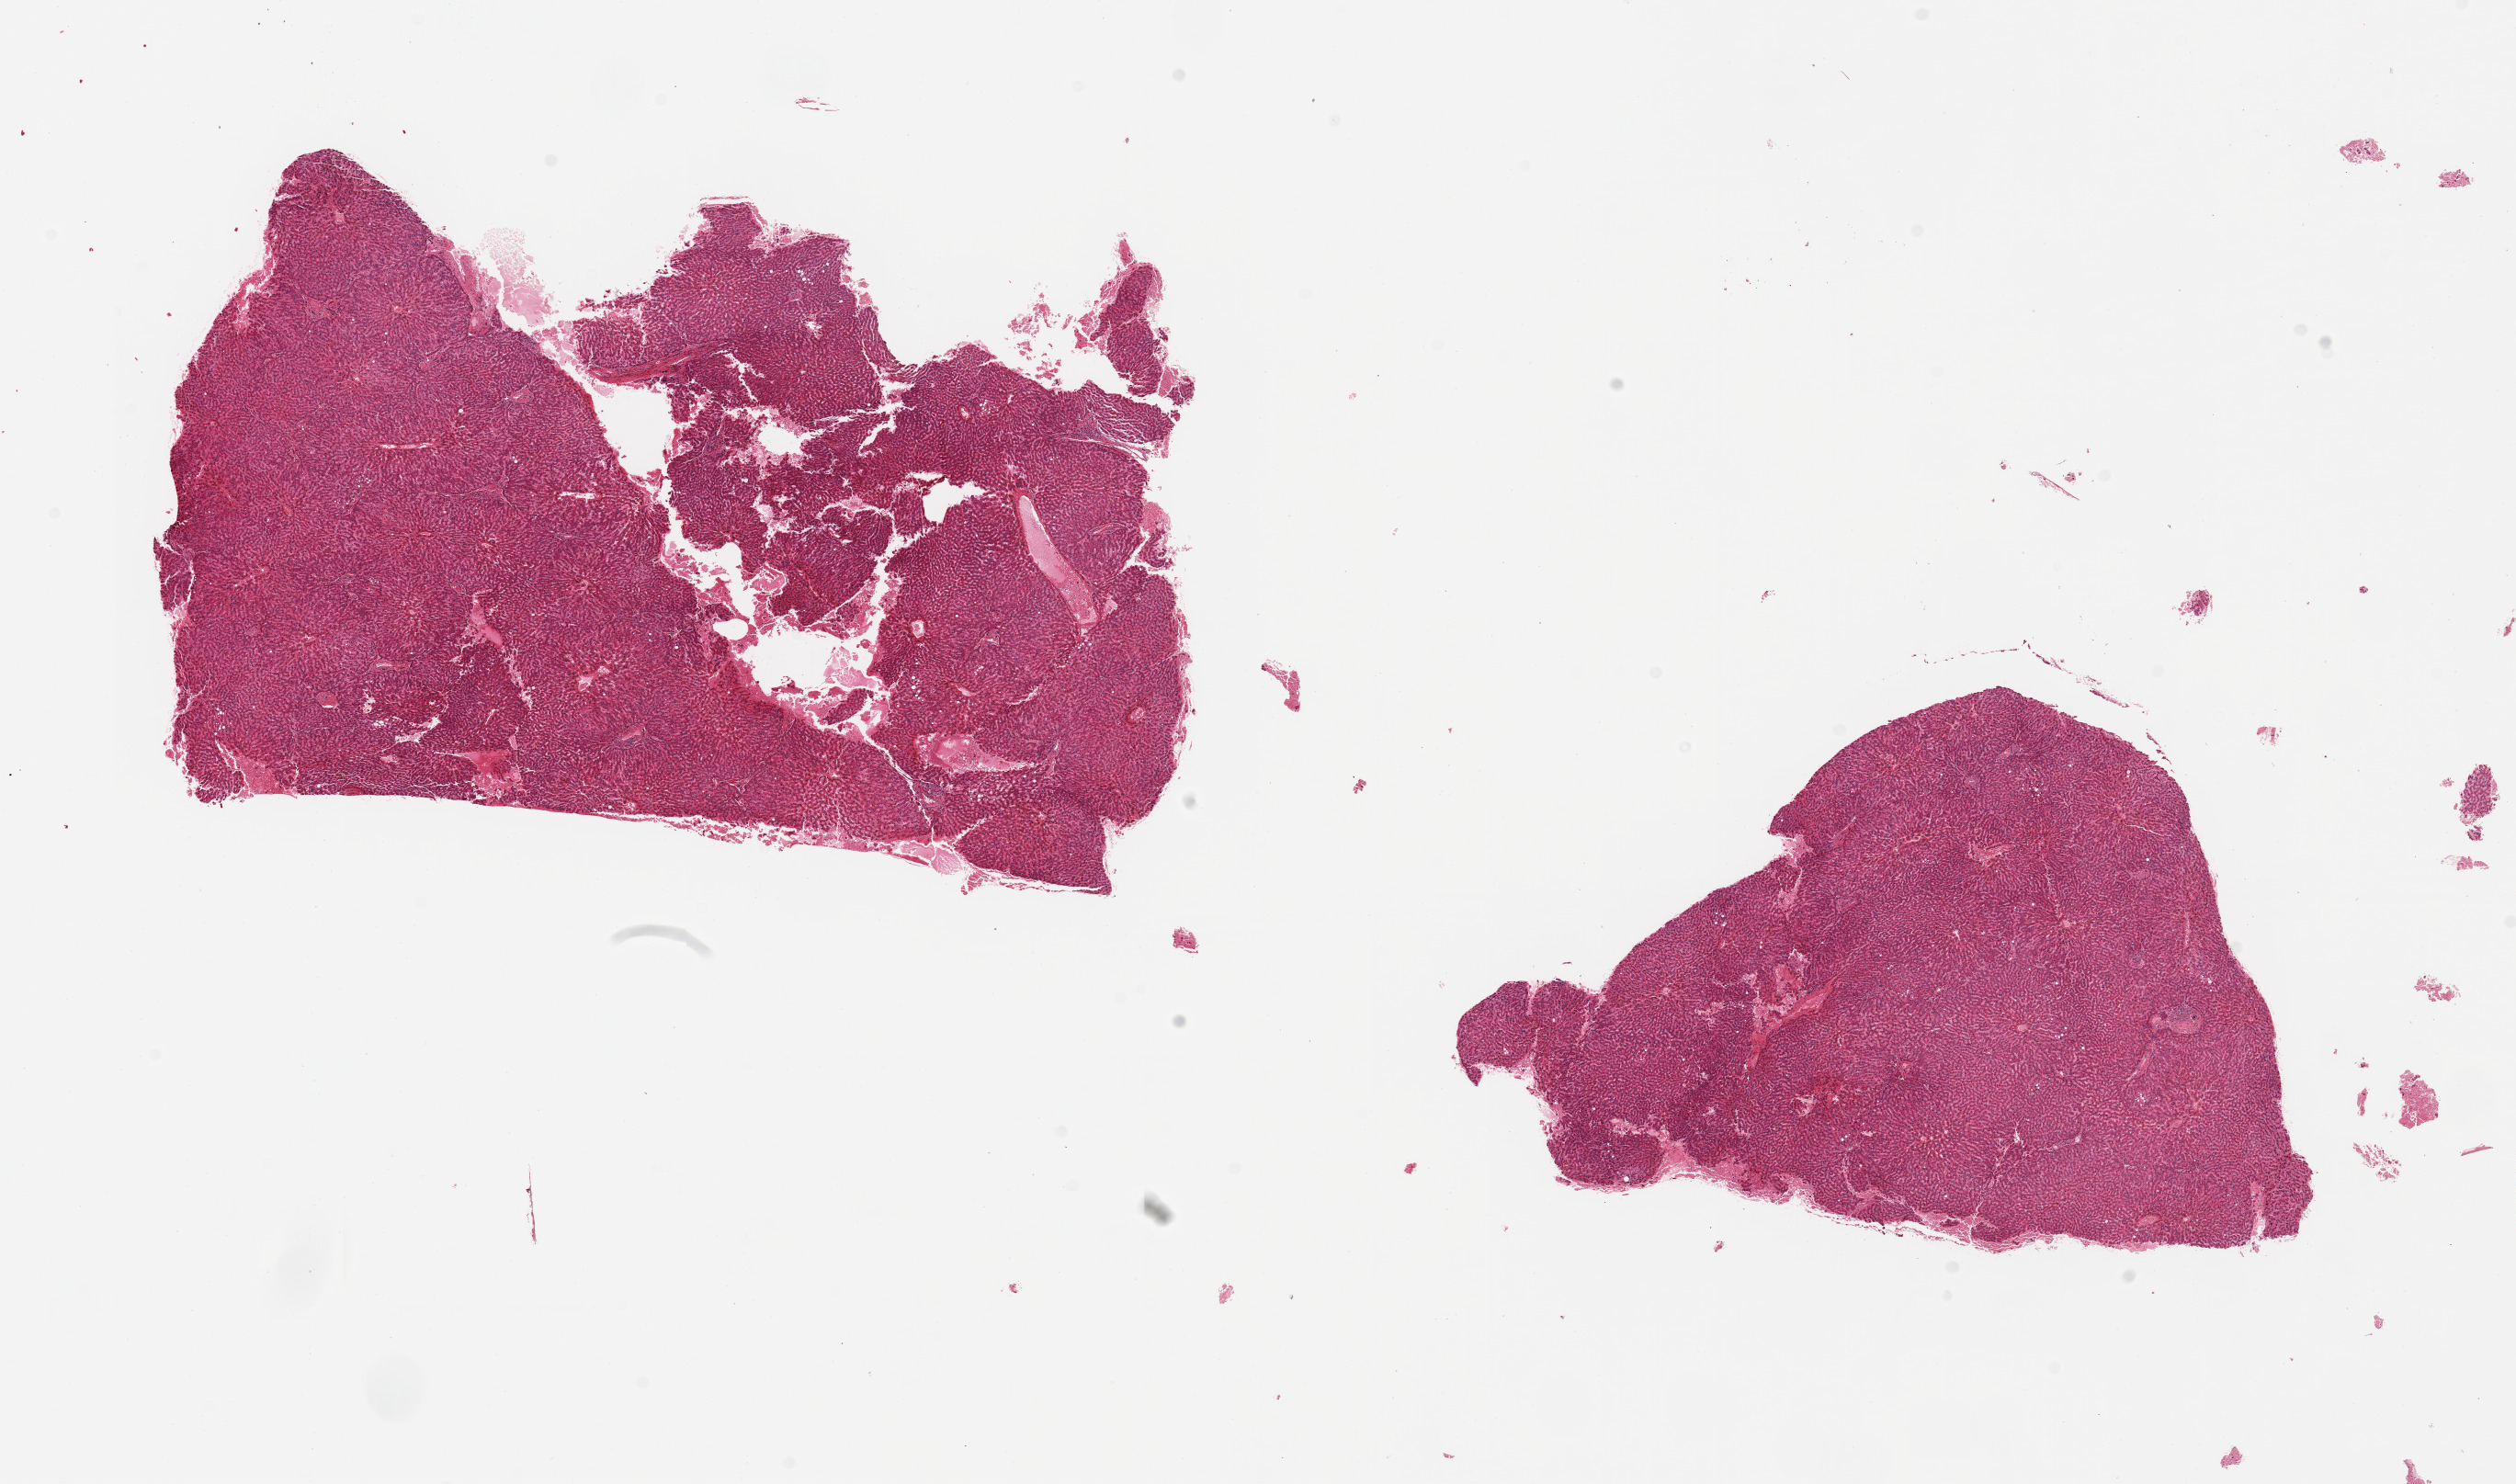
Digitized H&E-stained section, brightfield, a low-resolution overview of the entire scanned area, about 21.7 x 12.8 mm (from a 20x scan), PAXgene-fixed, paraffin-embedded tissue, target tissue: liver, tissue donor sample.
Pathologist's review note for this sample: 2 pieces, mild congestion.